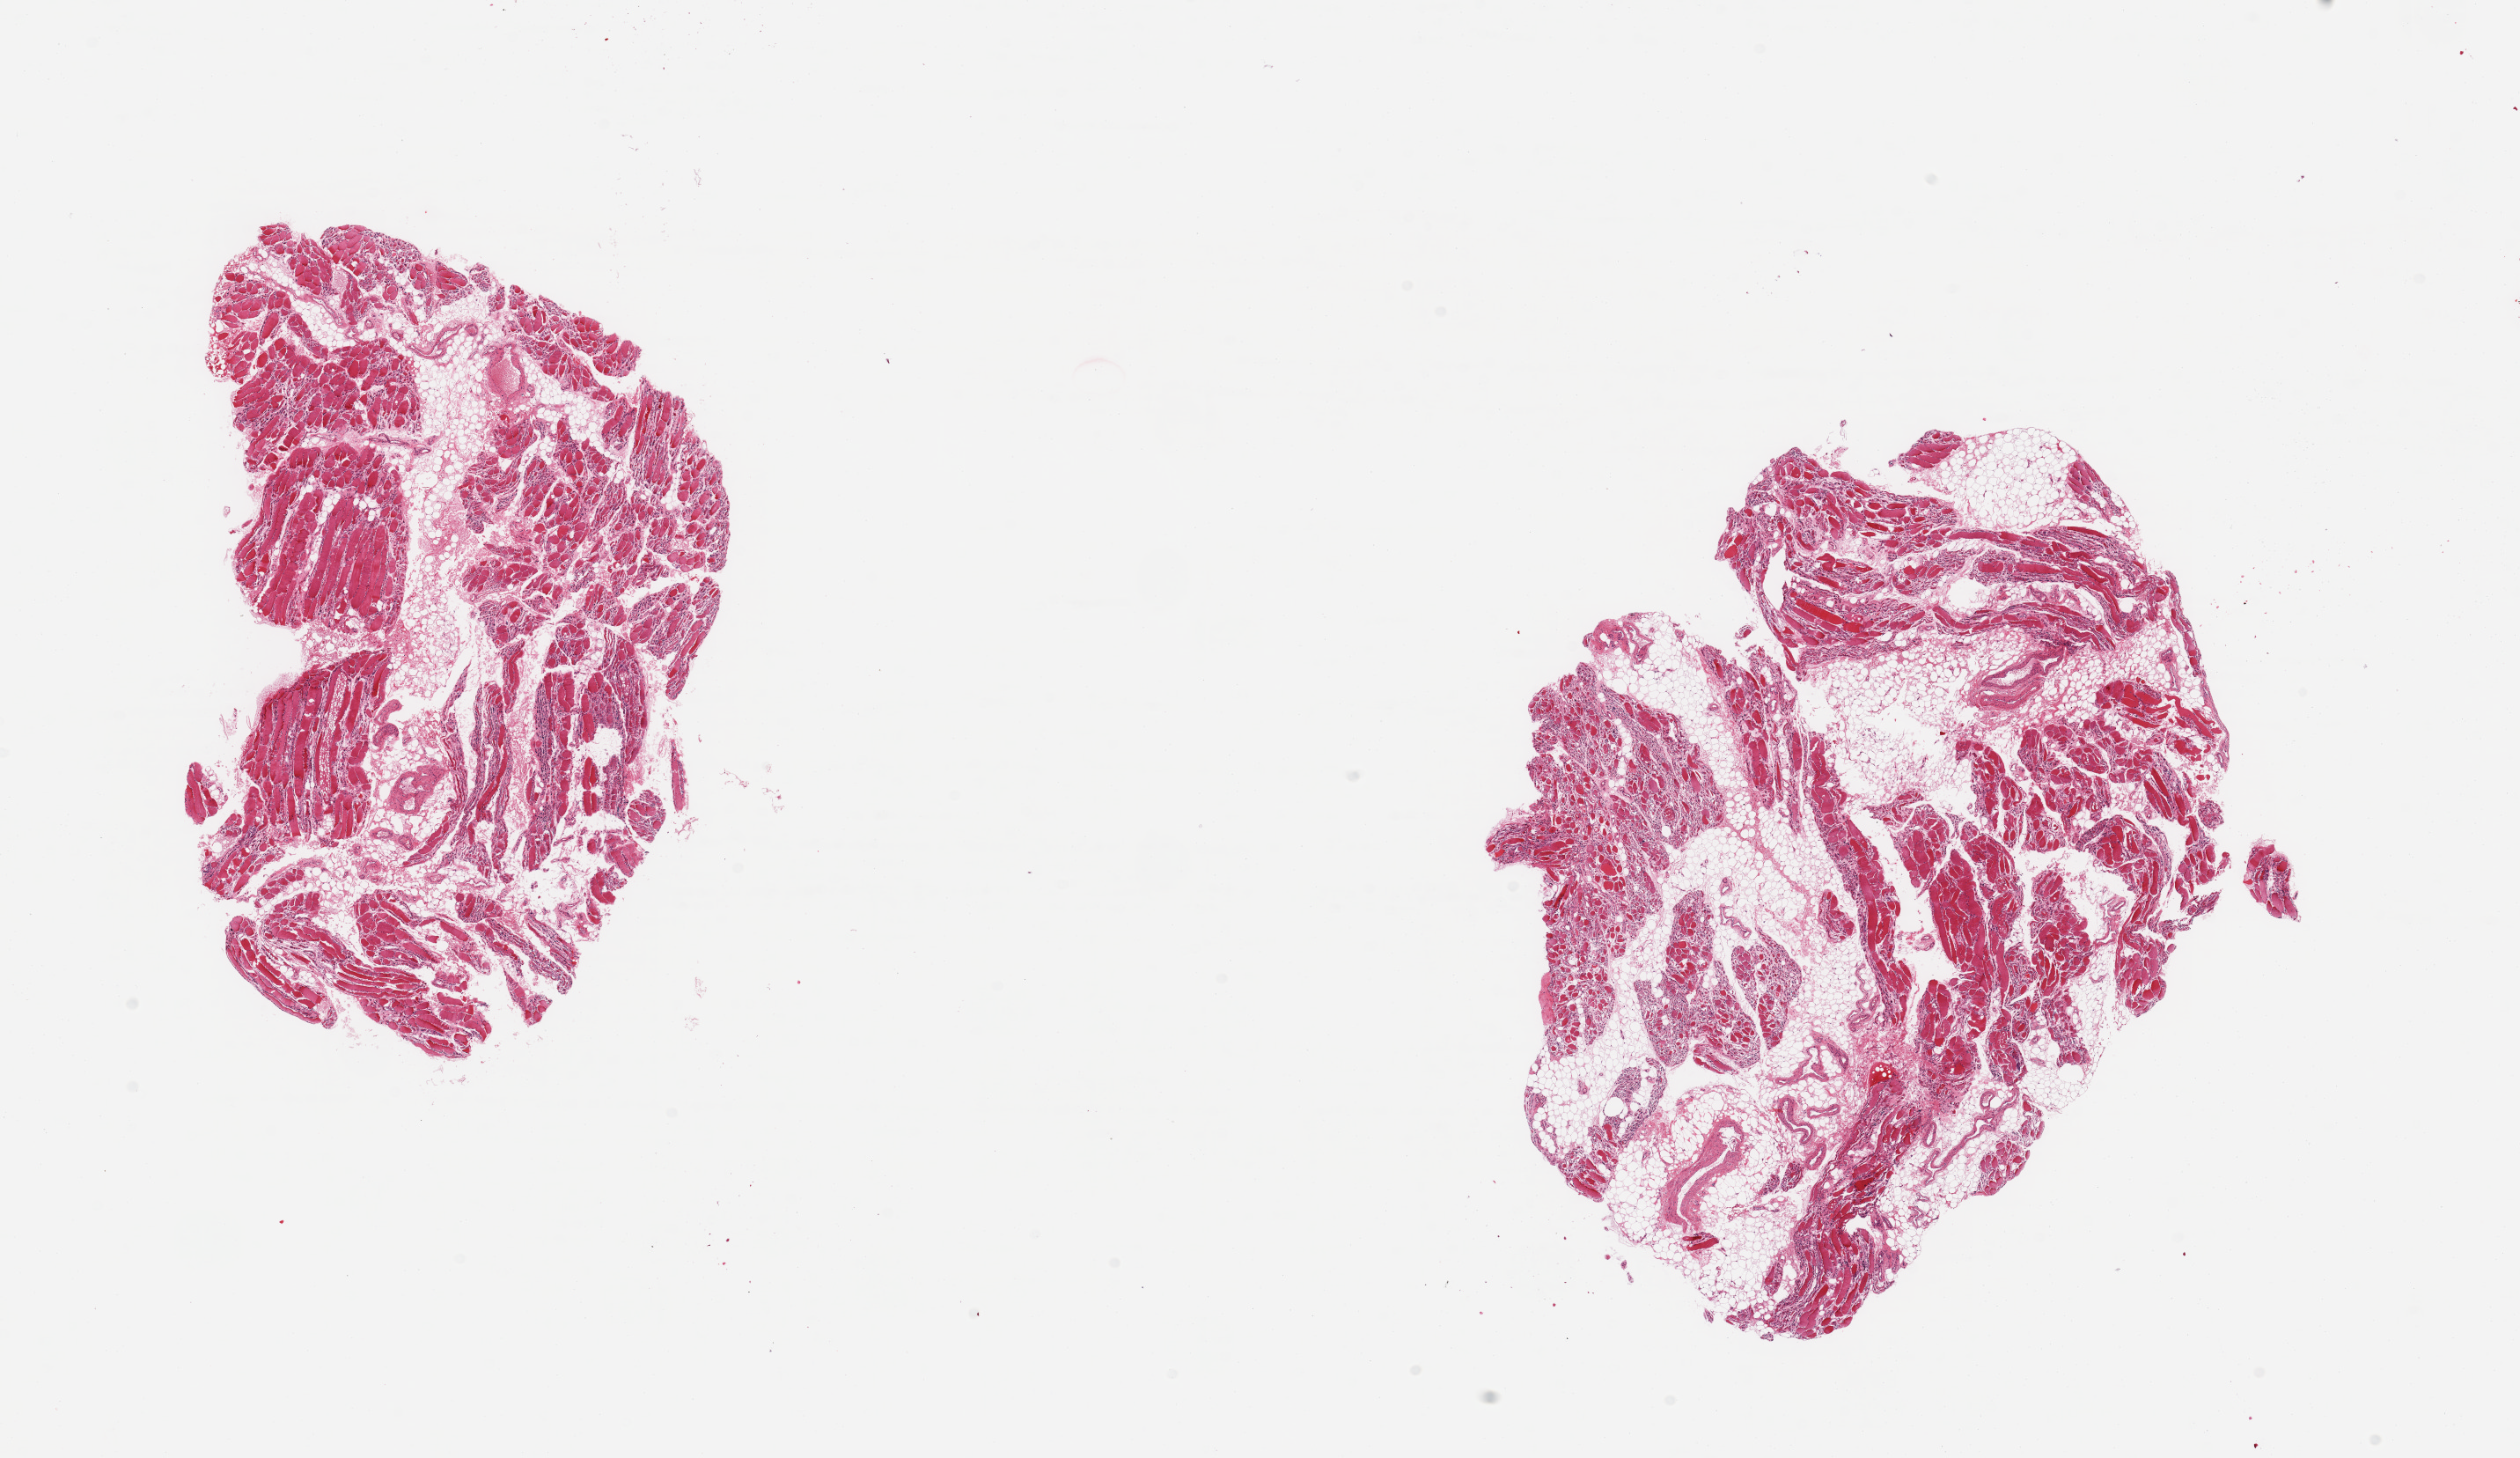
Whole-slide image, hematoxylin and eosin (H&E) stain, brightfield — shown as a low-resolution overview of the whole scanned area (about 22.6 x 13.1 mm, from a 20x scan), PAXgene-fixed paraffin-embedded (PFPE) section, sampled site (target tissue): skeletal muscle, donor tissue sample. Donor sex: male.
Reviewer comment on this tissue sample: 2 pieces; severe atrophy with 20% & 50% internal fat.